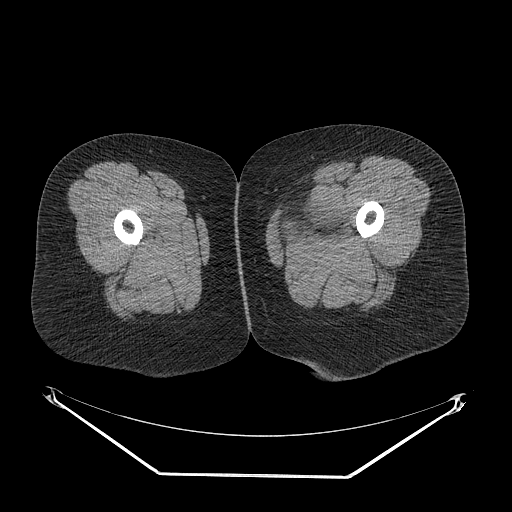
CT of an extremity soft-tissue mass (from a PET/CT study), one axial slice; slice 14 of 267 in the series (ordered by position); reconstruction kernel STANDARD; soft-tissue window (W 400 / L 40 HU); 512 × 512 image matrix, field of view 500 × 500 mm. Female patient. Case-level facts recorded for this patient, not image findings: histological type: myxofibrosarcoma; grade: intermediate; site of the primary tumour: left thigh.
Structures marked on this image (expert contour drawn on MRI and transferred to this co-registered scan by the dataset authors):
- gross tumour volume including surrounding oedema: bounding box (x1, y1, x2, y2) in pixels: (278, 201, 353, 243)
- gross tumour volume (mass): (313, 201, 337, 211)